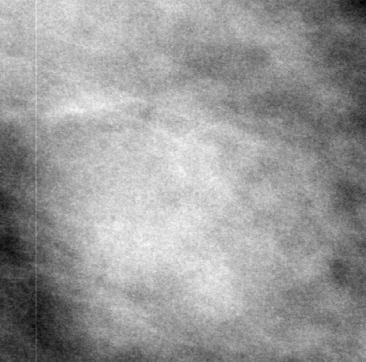
Crop from a digitized film mammogram around one marked abnormality, left breast, CC view.
Marked abnormality: mass, shape oval, margins obscured; BI-RADS assessment category 4; subtlety rating 4 on a 1 (subtle) to 5 (obvious) scale; pathology result (as recorded, not read from the image): benign.